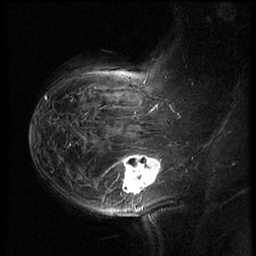
Breast MRI (dynamic contrast-enhanced), one sagittal slice. Position 45 of 62 along the scan axis. 3 images stored at this slice position (order not interpretable as contrast timing). 1.5 T. TE 4.2 ms, TR 8.9 ms. 2.5 mm slice thickness. 256 × 256 image matrix, field of view 200 × 200 mm. Patient: female, 37 years. Case-level facts recorded for this patient, not image findings: setting: breast cancer imaged before/during neoadjuvant chemotherapy; receptor status: triple-negative.
Outlined on this slice (semi-automatically segmented with operator editing):
- analysis volume of interest (the breast-tissue region the enhancement analysis was run in; not a lesion): bounding box [x1, y1, x2, y2] px = [116, 146, 168, 203]
- tumour enhancement mask (voxels above the 140 % enhancement threshold inside the analysis volume of interest): [121, 155, 160, 194]